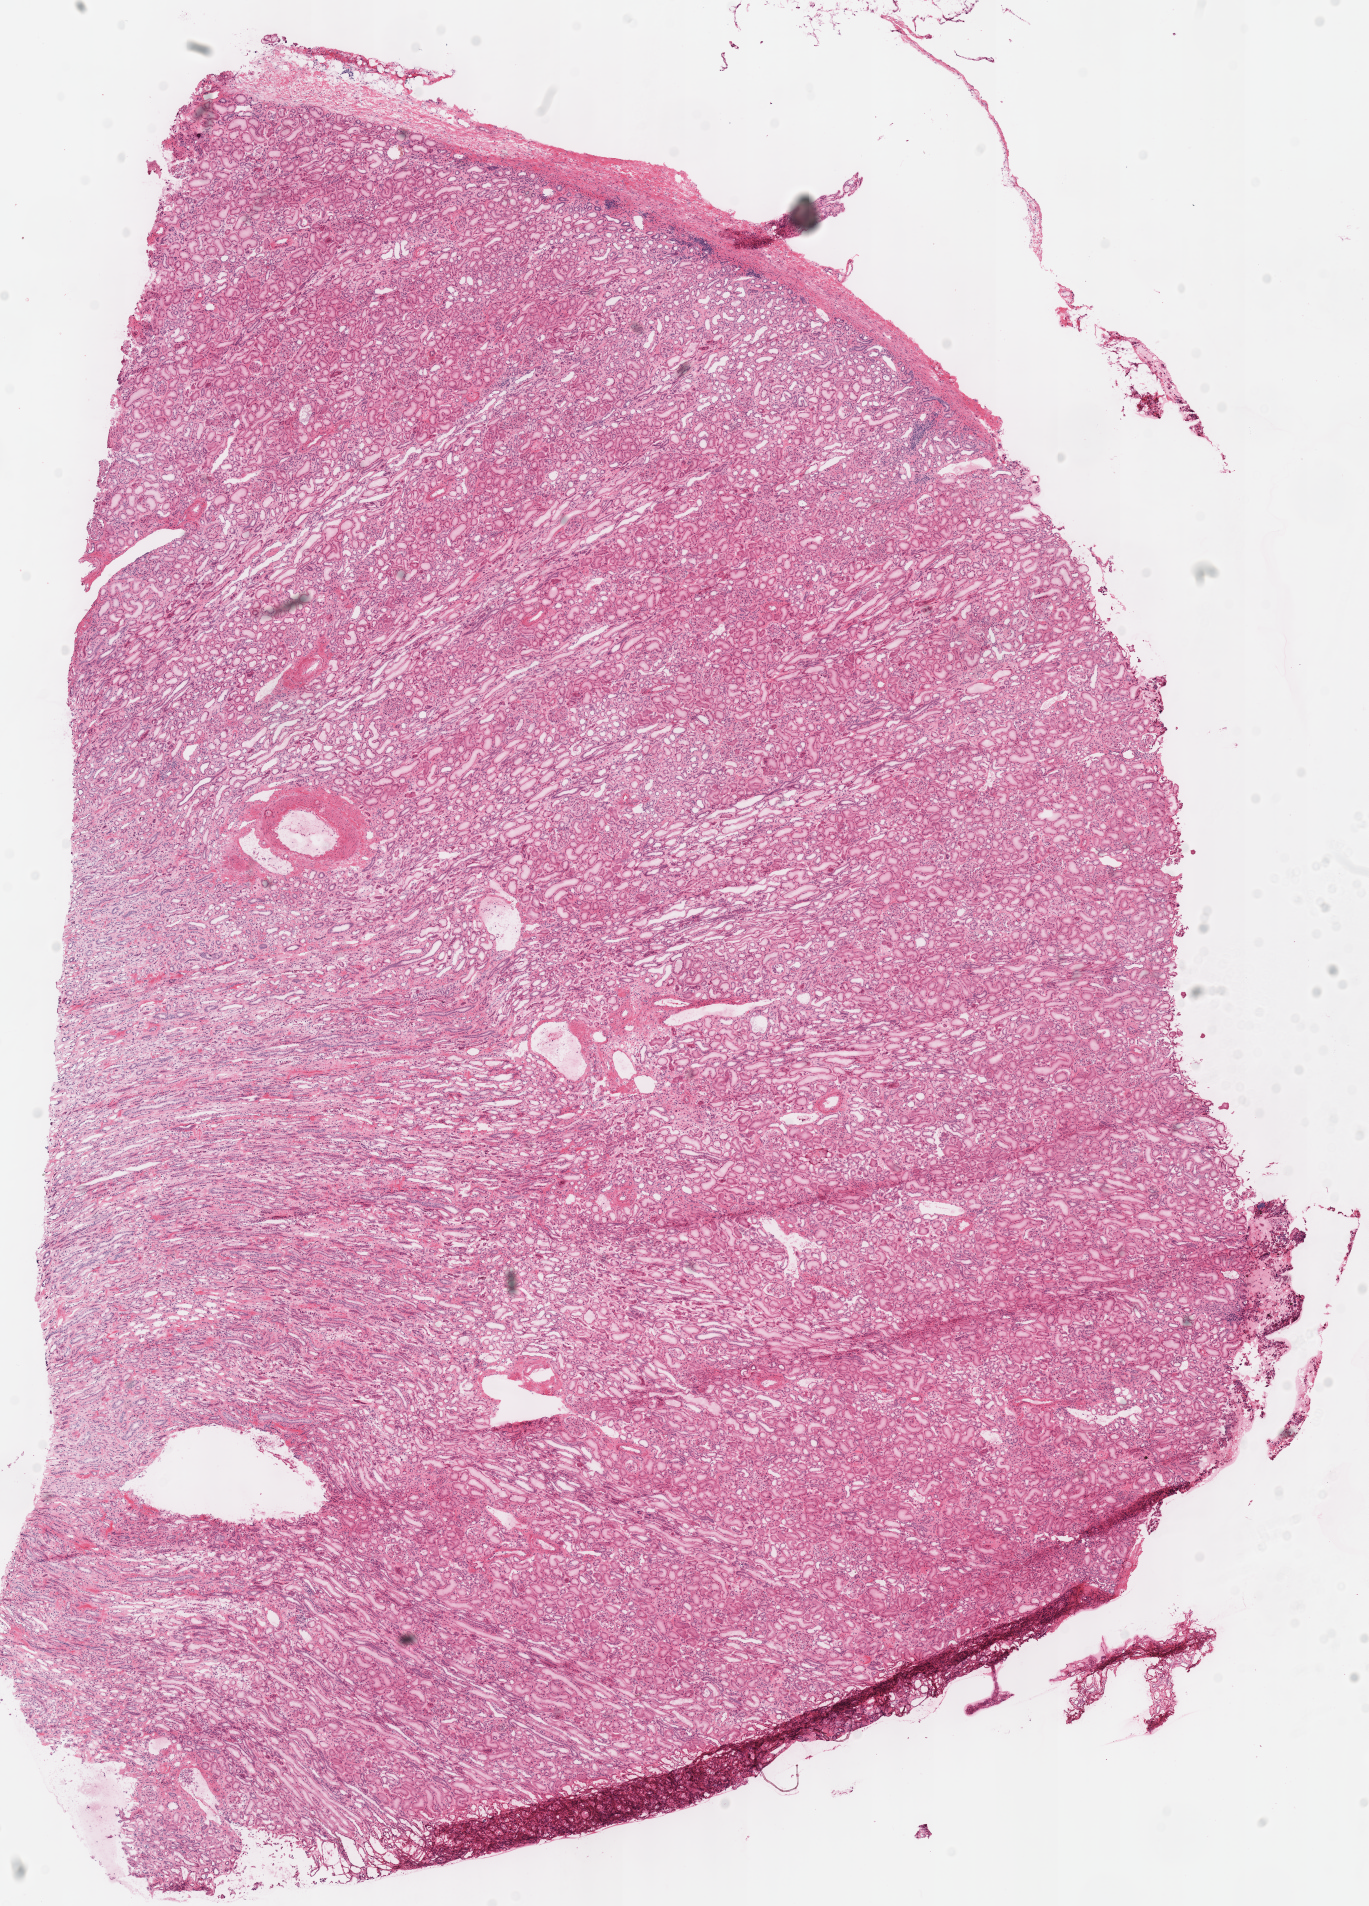
Whole-slide histology image, Hematoxylin and eosin (H&E) stained, whole scanned area (about 10.8 x 15.0 mm) shown as a low-resolution overview; frozen section; sample: solid tissue normal (non-tumour tissue), kidney. Male, age 67 years at initial diagnosis.
This section: solid tissue normal (non-tumour) sample from the same patient. Patient diagnosis: Renal cell carcinoma, chromophobe type.